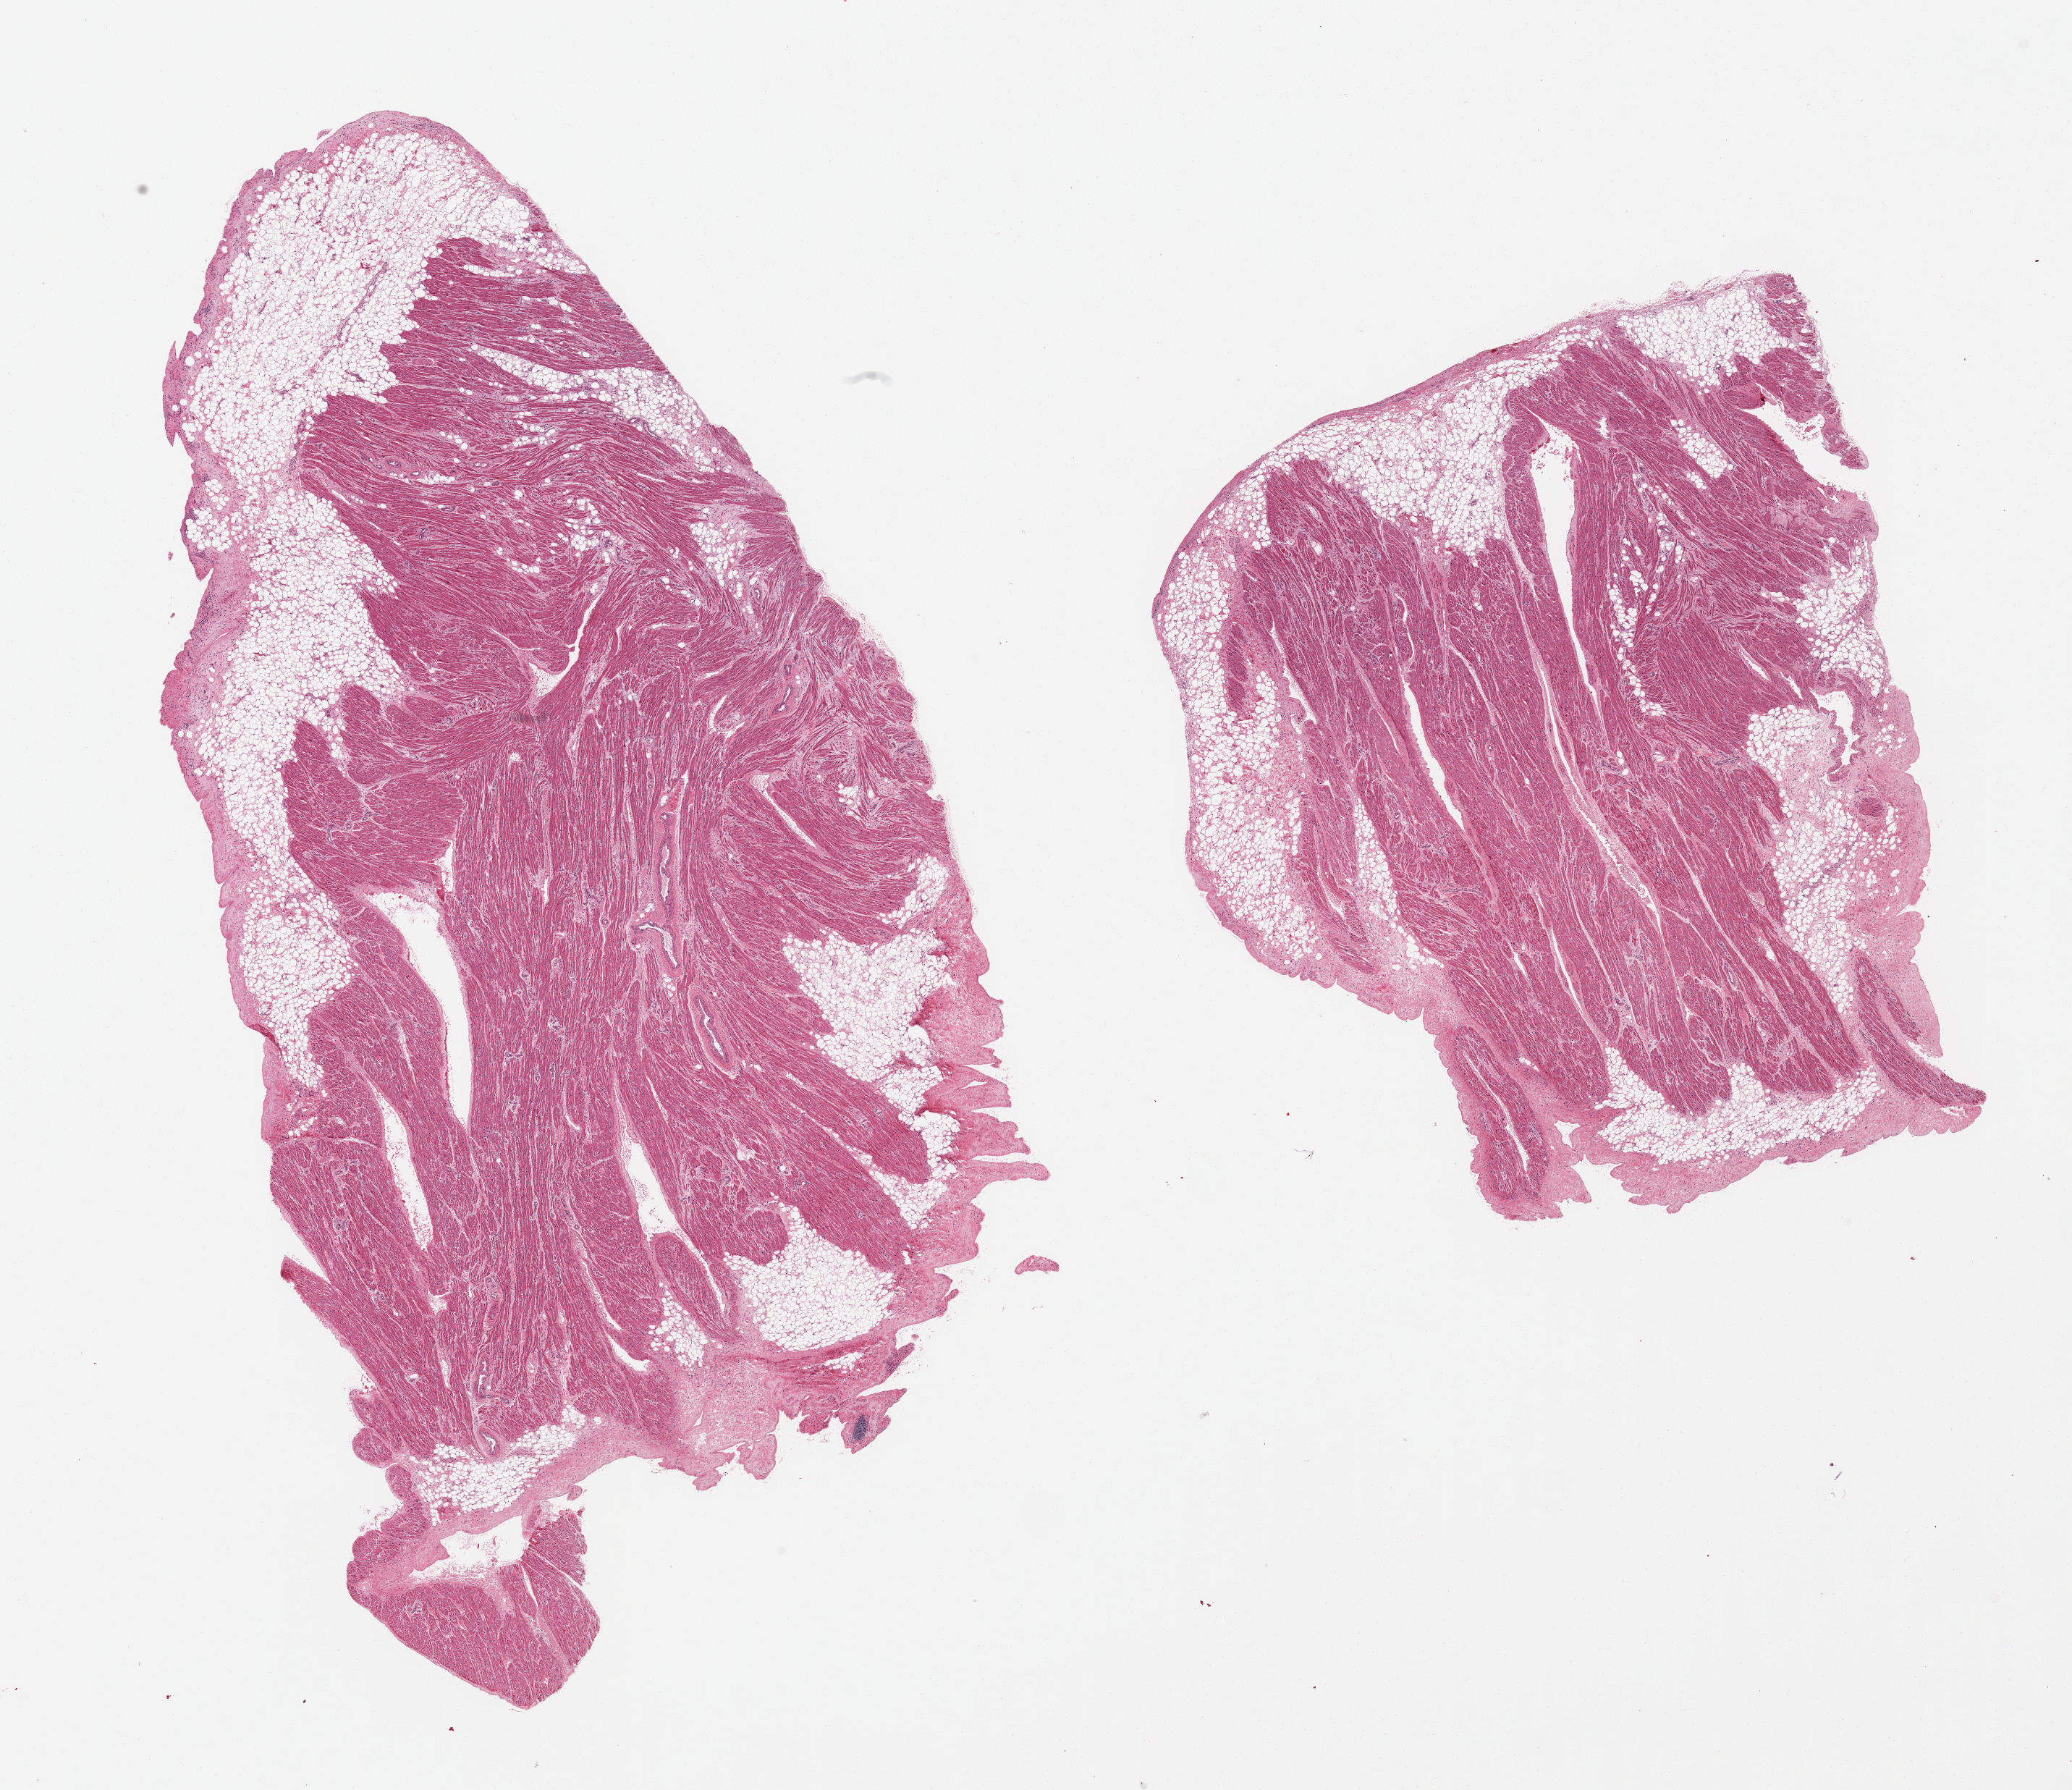
H&E whole-slide image, a low-resolution overview of the entire scanned area, about 22.6 x 19.6 mm; PAXgene-fixed, paraffin-embedded tissue; sampled site (target tissue): auricular appendage; donor tissue sample. Female donor.
• review note (as recorded): 2 pieces, no abnormalities